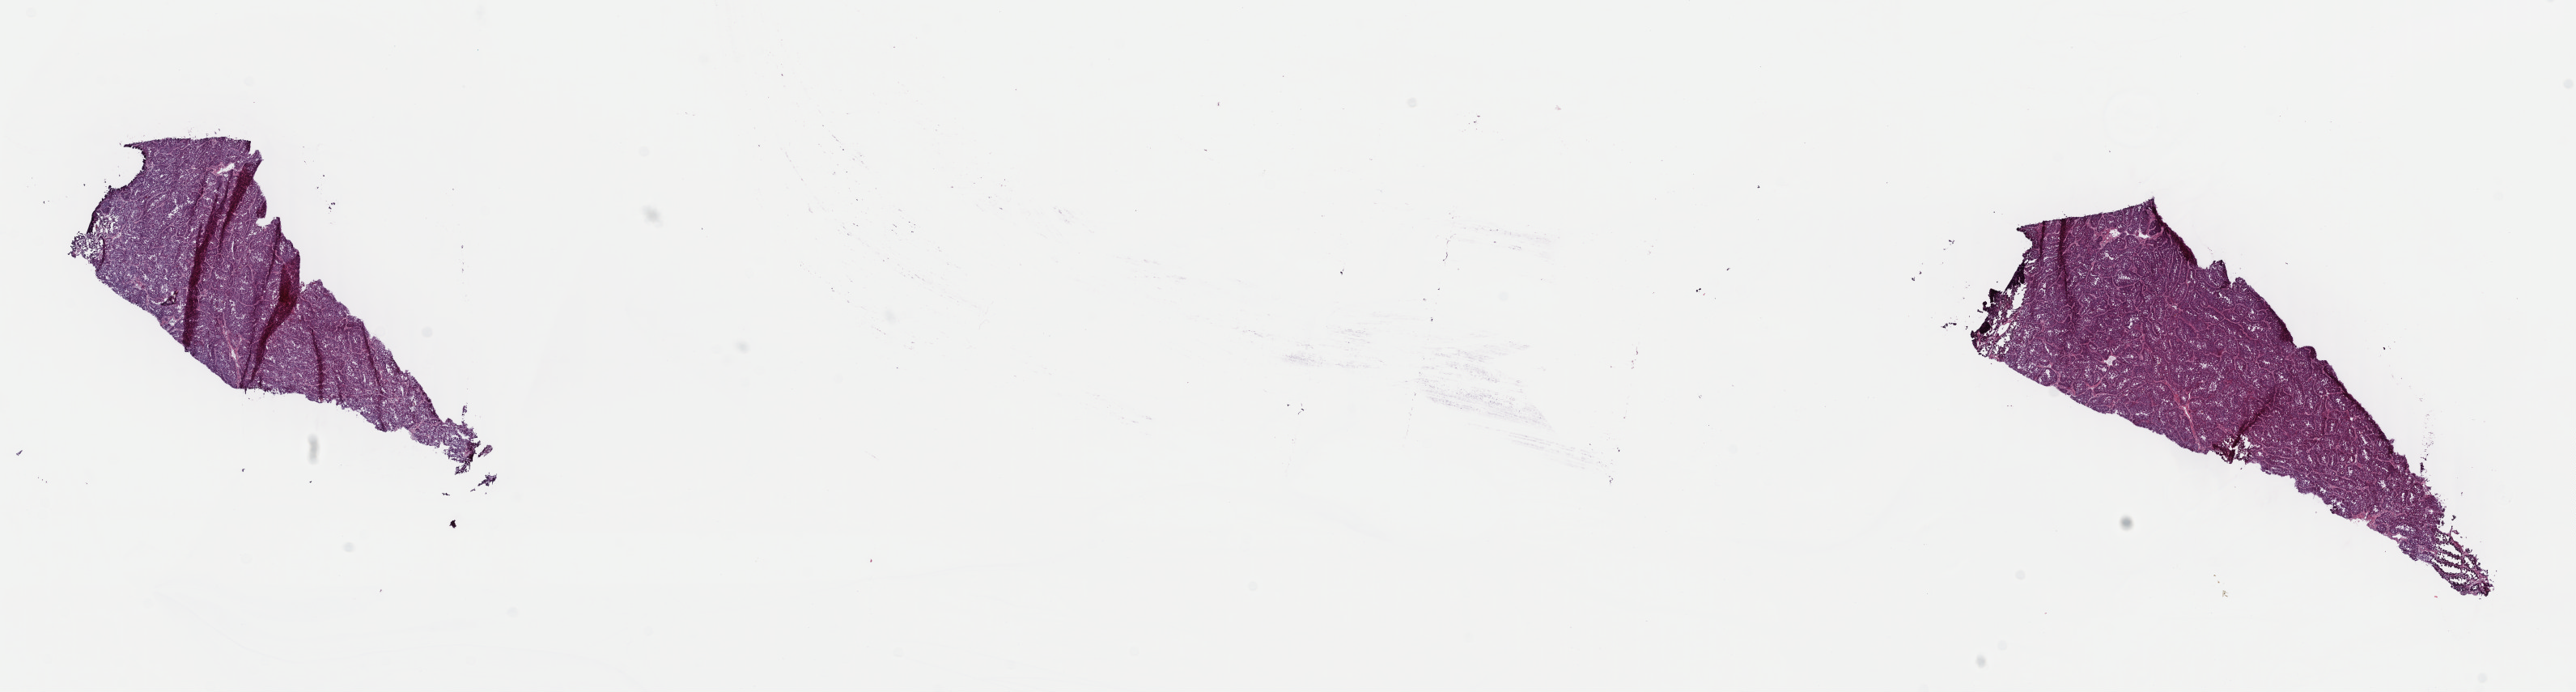
H&E whole-slide image, shown as a low-resolution overview of the whole scanned area (about 25.1 x 6.7 mm). Frozen section from the top of the tissue portion. Sample: primary tumour, kidney. Male, age 62 years at initial diagnosis. Composition of this section per pathologist review: tumour cells 90%, tumour nuclei 90%, normal cells 0%, stromal cells 10%, necrosis 0%. Infiltration values recorded for this section: lymphocyte infiltration 0%, monocyte infiltration 0%, neutrophil infiltration 0%.
• TNM: T1a NX MX
• pathologic diagnosis: Papillary adenocarcinoma, NOS
• AJCC pathologic stage: I (7th edition)